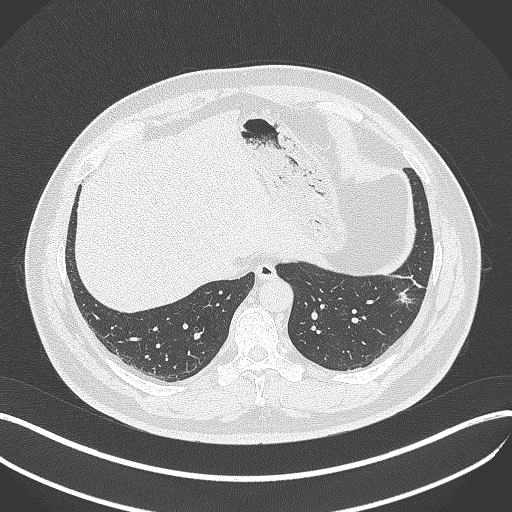
Chest CT, one axial slice. Slice 106 of 429 in the series (ordered by position). Lung window (W 1500 / L -600 HU). 1 mm slice thickness. 512 × 512 image matrix. Patient: male, 39 years. From the clinical record (not read from this slice): clinical TNM (as recorded): T2a N0 M0; histopathological grade: G2-3.
Outlined on this slice (bounding box drawn by a radiologist):
- lung tumour (recorded histology: adenocarcinoma): bounding box <393,282,417,307> (left, top, right, bottom; pixels)